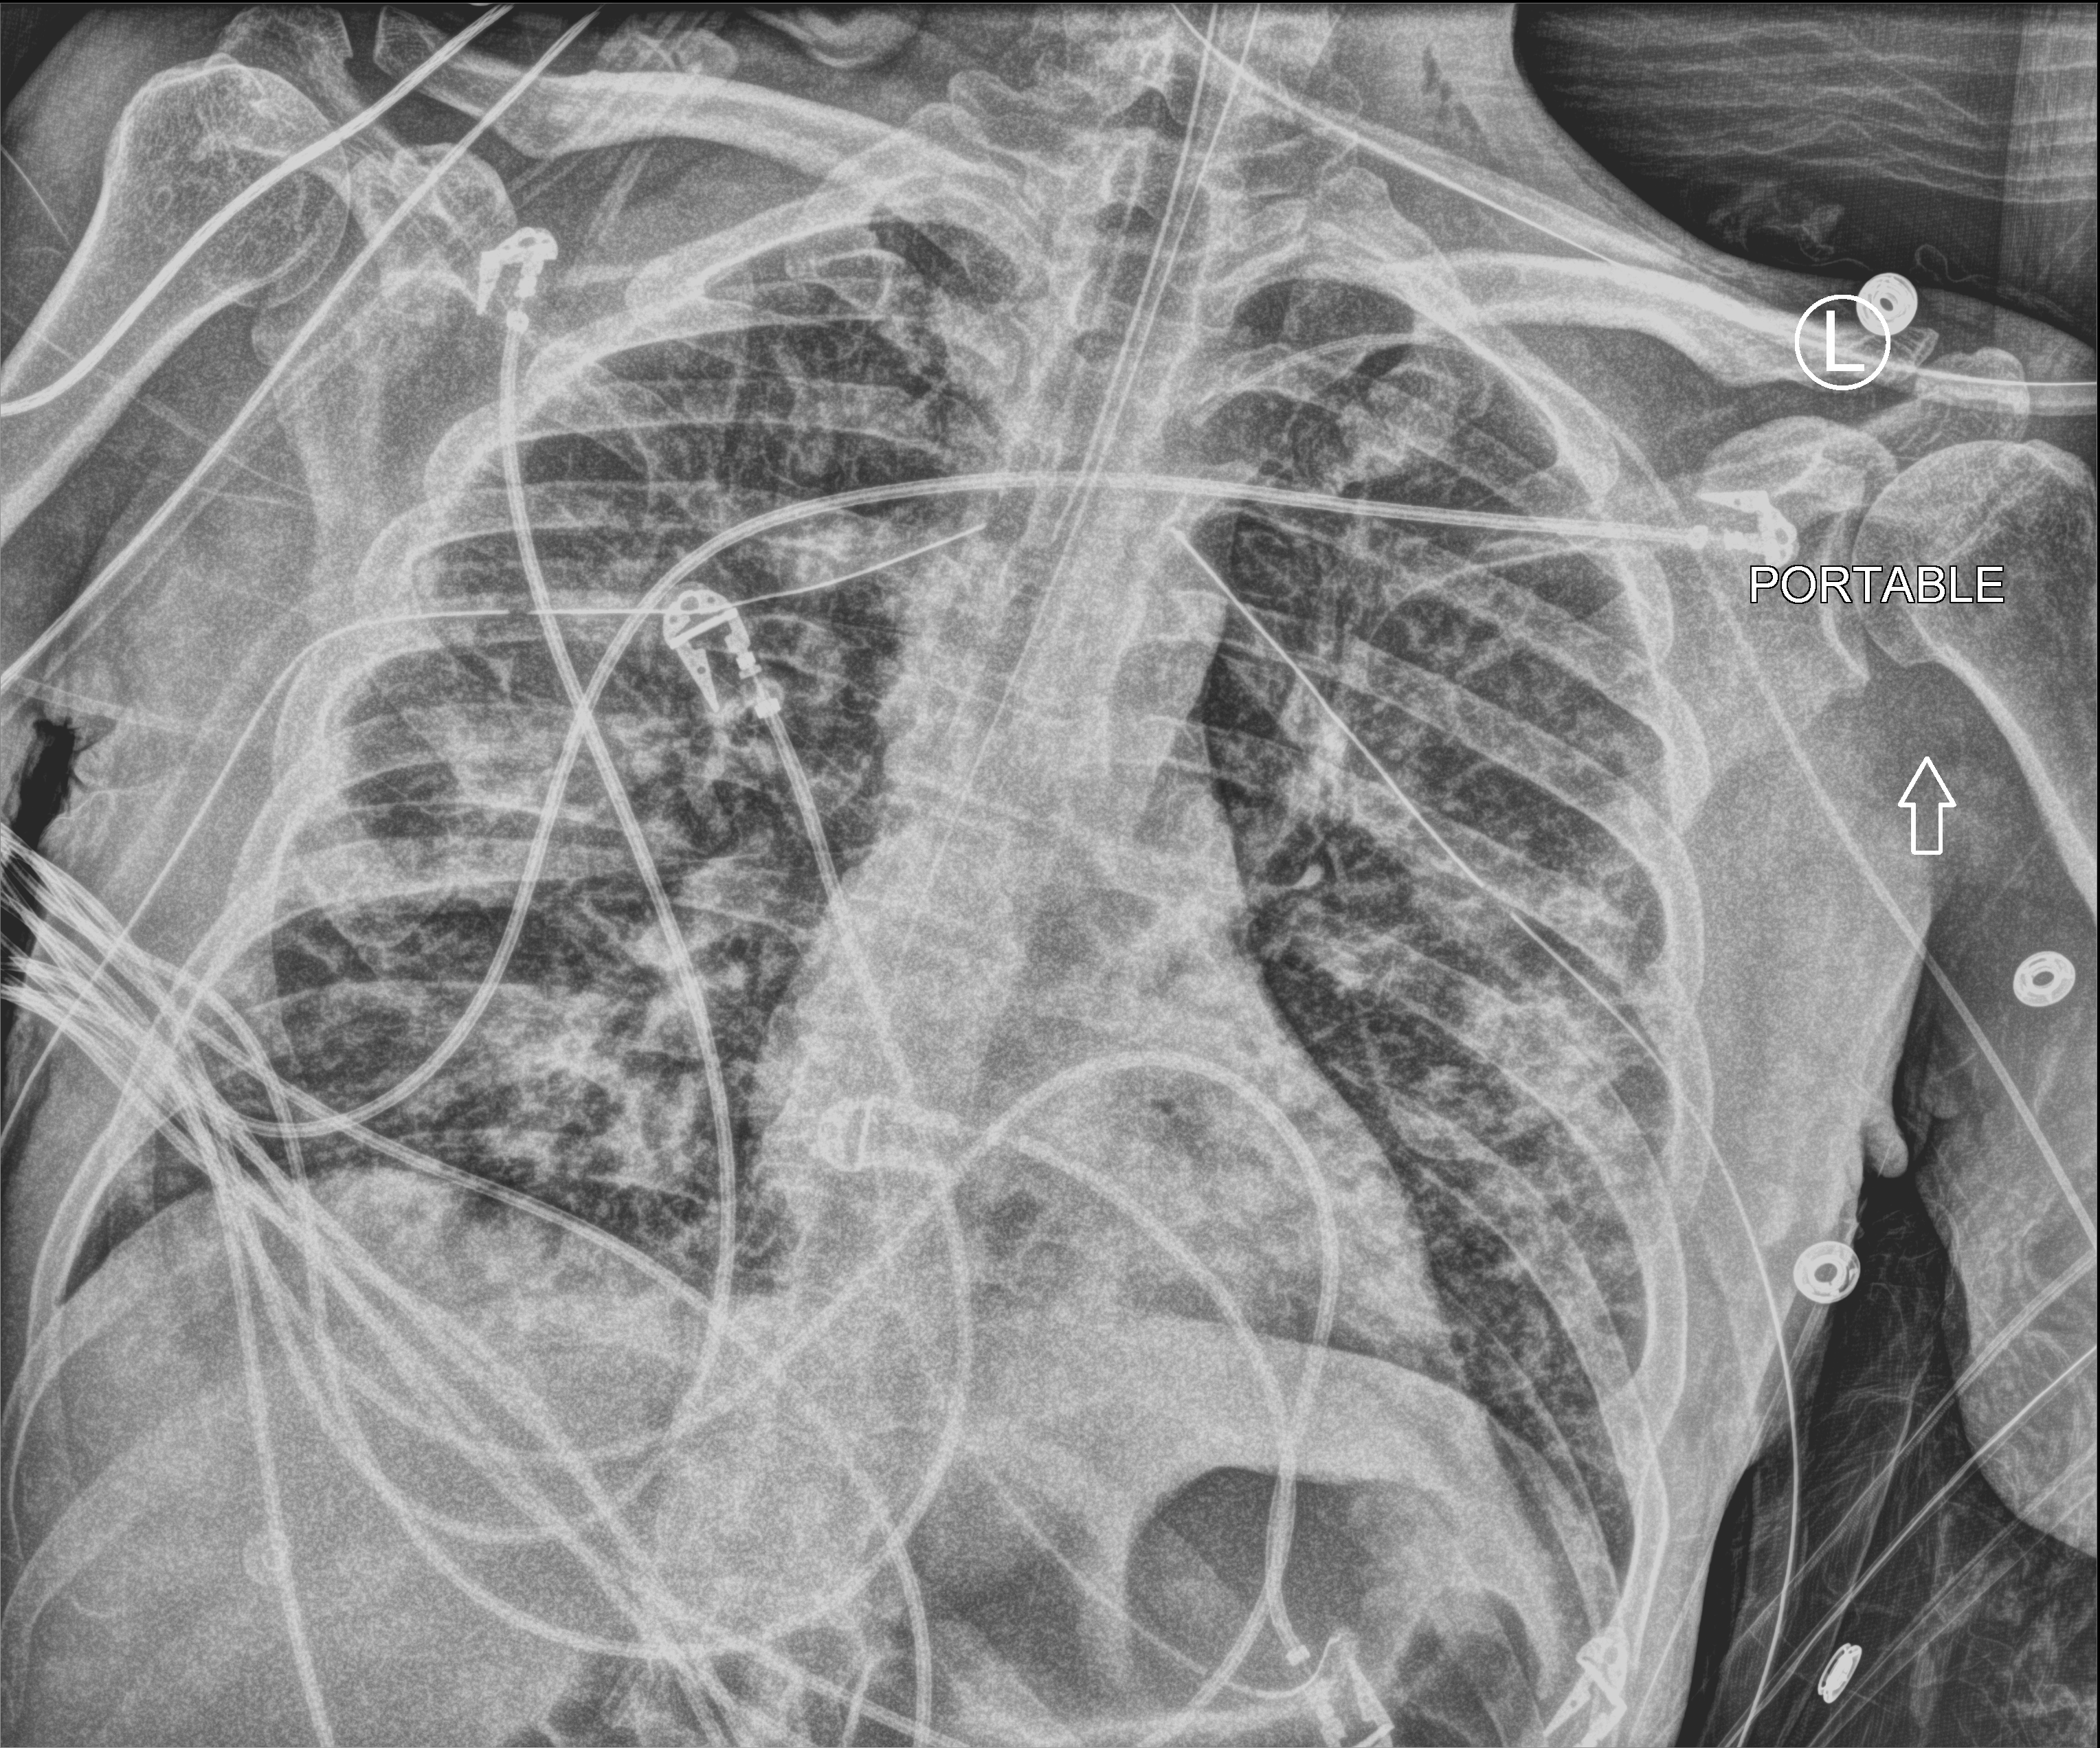
Bedside chest radiograph (computed radiography); anteroposterior (AP) projection. Male patient hospitalised with COVID-19, age 18–59 years.
Admission-level facts for this patient (not findings on this image; timing relative to this image not recorded):
- length of hospital stay: 96 days